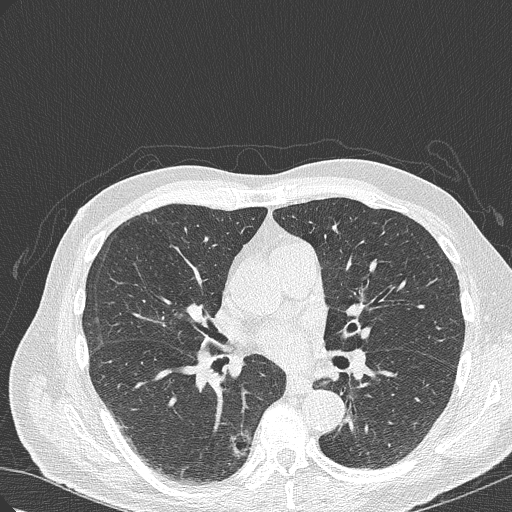
Chest CT (low-dose screening protocol), one axial image. First (baseline) screen. Lung window (W 1500 / L -600 HU). Lung (sharp) reconstruction kernel (B50f). Slice 149 of 322 in the series. 512 × 512 image matrix, field of view 350 × 350 mm. Male, age 70 years at enrolment. Current smoker at enrolment.
Expert-annotated lung lesion, bounding box [x1, y1, x2, y2] px = [198, 420, 261, 481]. The screening reader recorded 4 non-calcified nodules or masses ≥4 mm on this exam (right lower lobe, right lower lobe, right upper lobe, right lower lobe); which of them this box marks is not recorded. Official screen result: positive, change unspecified: nodule(s) >= 4 mm or enlarging nodule(s), mass(es), or other non-specific abnormalities suspicious for lung cancer. Later outcome: lung cancer diagnosed 978 days after this screen (after the third annual screen) — bronchiolo-alveolar adenocarcinoma, NOS, right lower lobe, poorly differentiated (G3), stage IB (AJCC 6th edition), 30 mm at pathology.